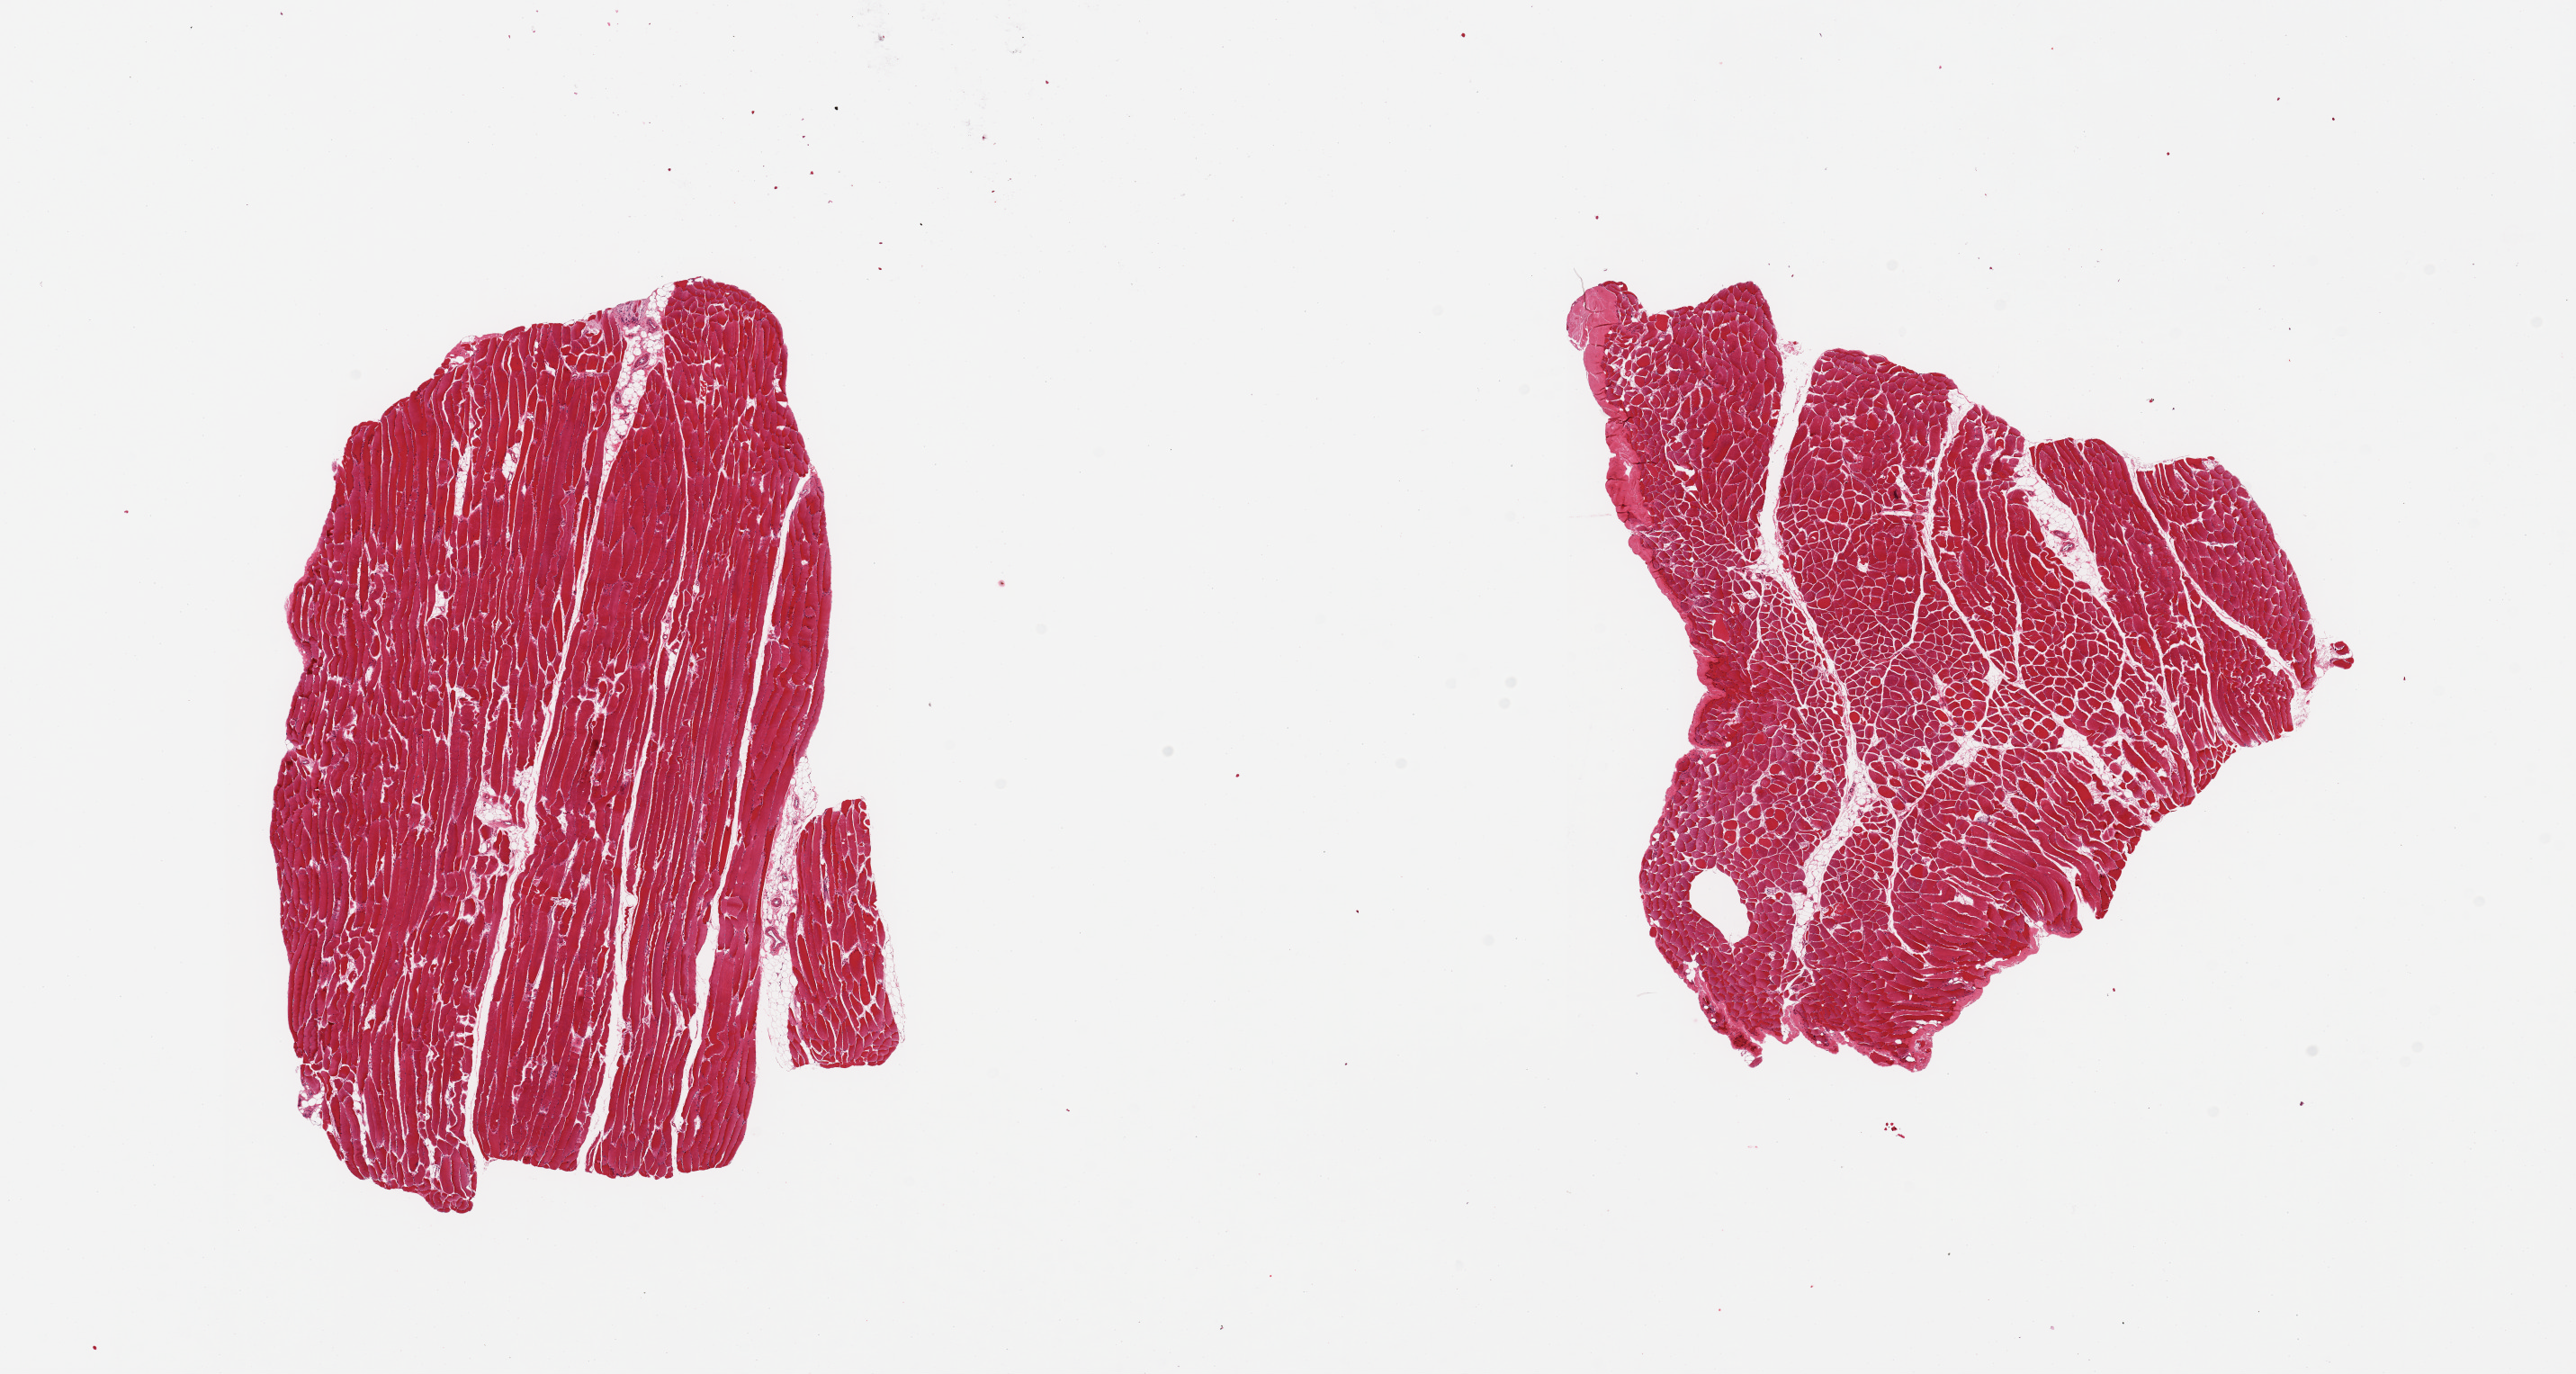
Digitized hematoxylin and eosin (H&E)-stained section, low-resolution overview of the scanned area, about 22.6 x 12.1 mm, PAXgene-fixed paraffin-embedded (PFPE) section, target tissue: skeletal muscle, donor tissue sample. Donor: female.
• reviewer comment on this tissue sample: 2 pieces; minimal internal fat